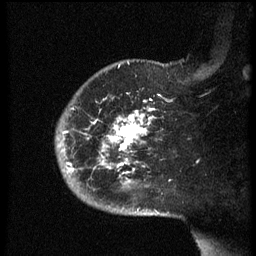
Breast MRI (dynamic contrast-enhanced), one sagittal slice; position 48 of 60 along the scan axis; dynamic contrast-enhanced series, image 2 of 3 at this slice position (ordered by acquisition); 1.5 T; TE 4.2 ms, TR 8.4 ms; 2.5 mm slice thickness; 256 × 256 image matrix. Female patient, age 38 years. Case-level facts recorded for this patient, not image findings: setting: breast cancer imaged before/during neoadjuvant chemotherapy; receptor status: HER2-positive.
Structures marked on this image (semi-automatically segmented with operator editing):
- analysis volume of interest (the breast-tissue region the enhancement analysis was run in; not a lesion): bounding box [x1, y1, x2, y2] px = [57, 74, 170, 202]
- tumour enhancement mask (voxels above the 70 % enhancement threshold inside the analysis volume of interest): [63, 109, 157, 186]